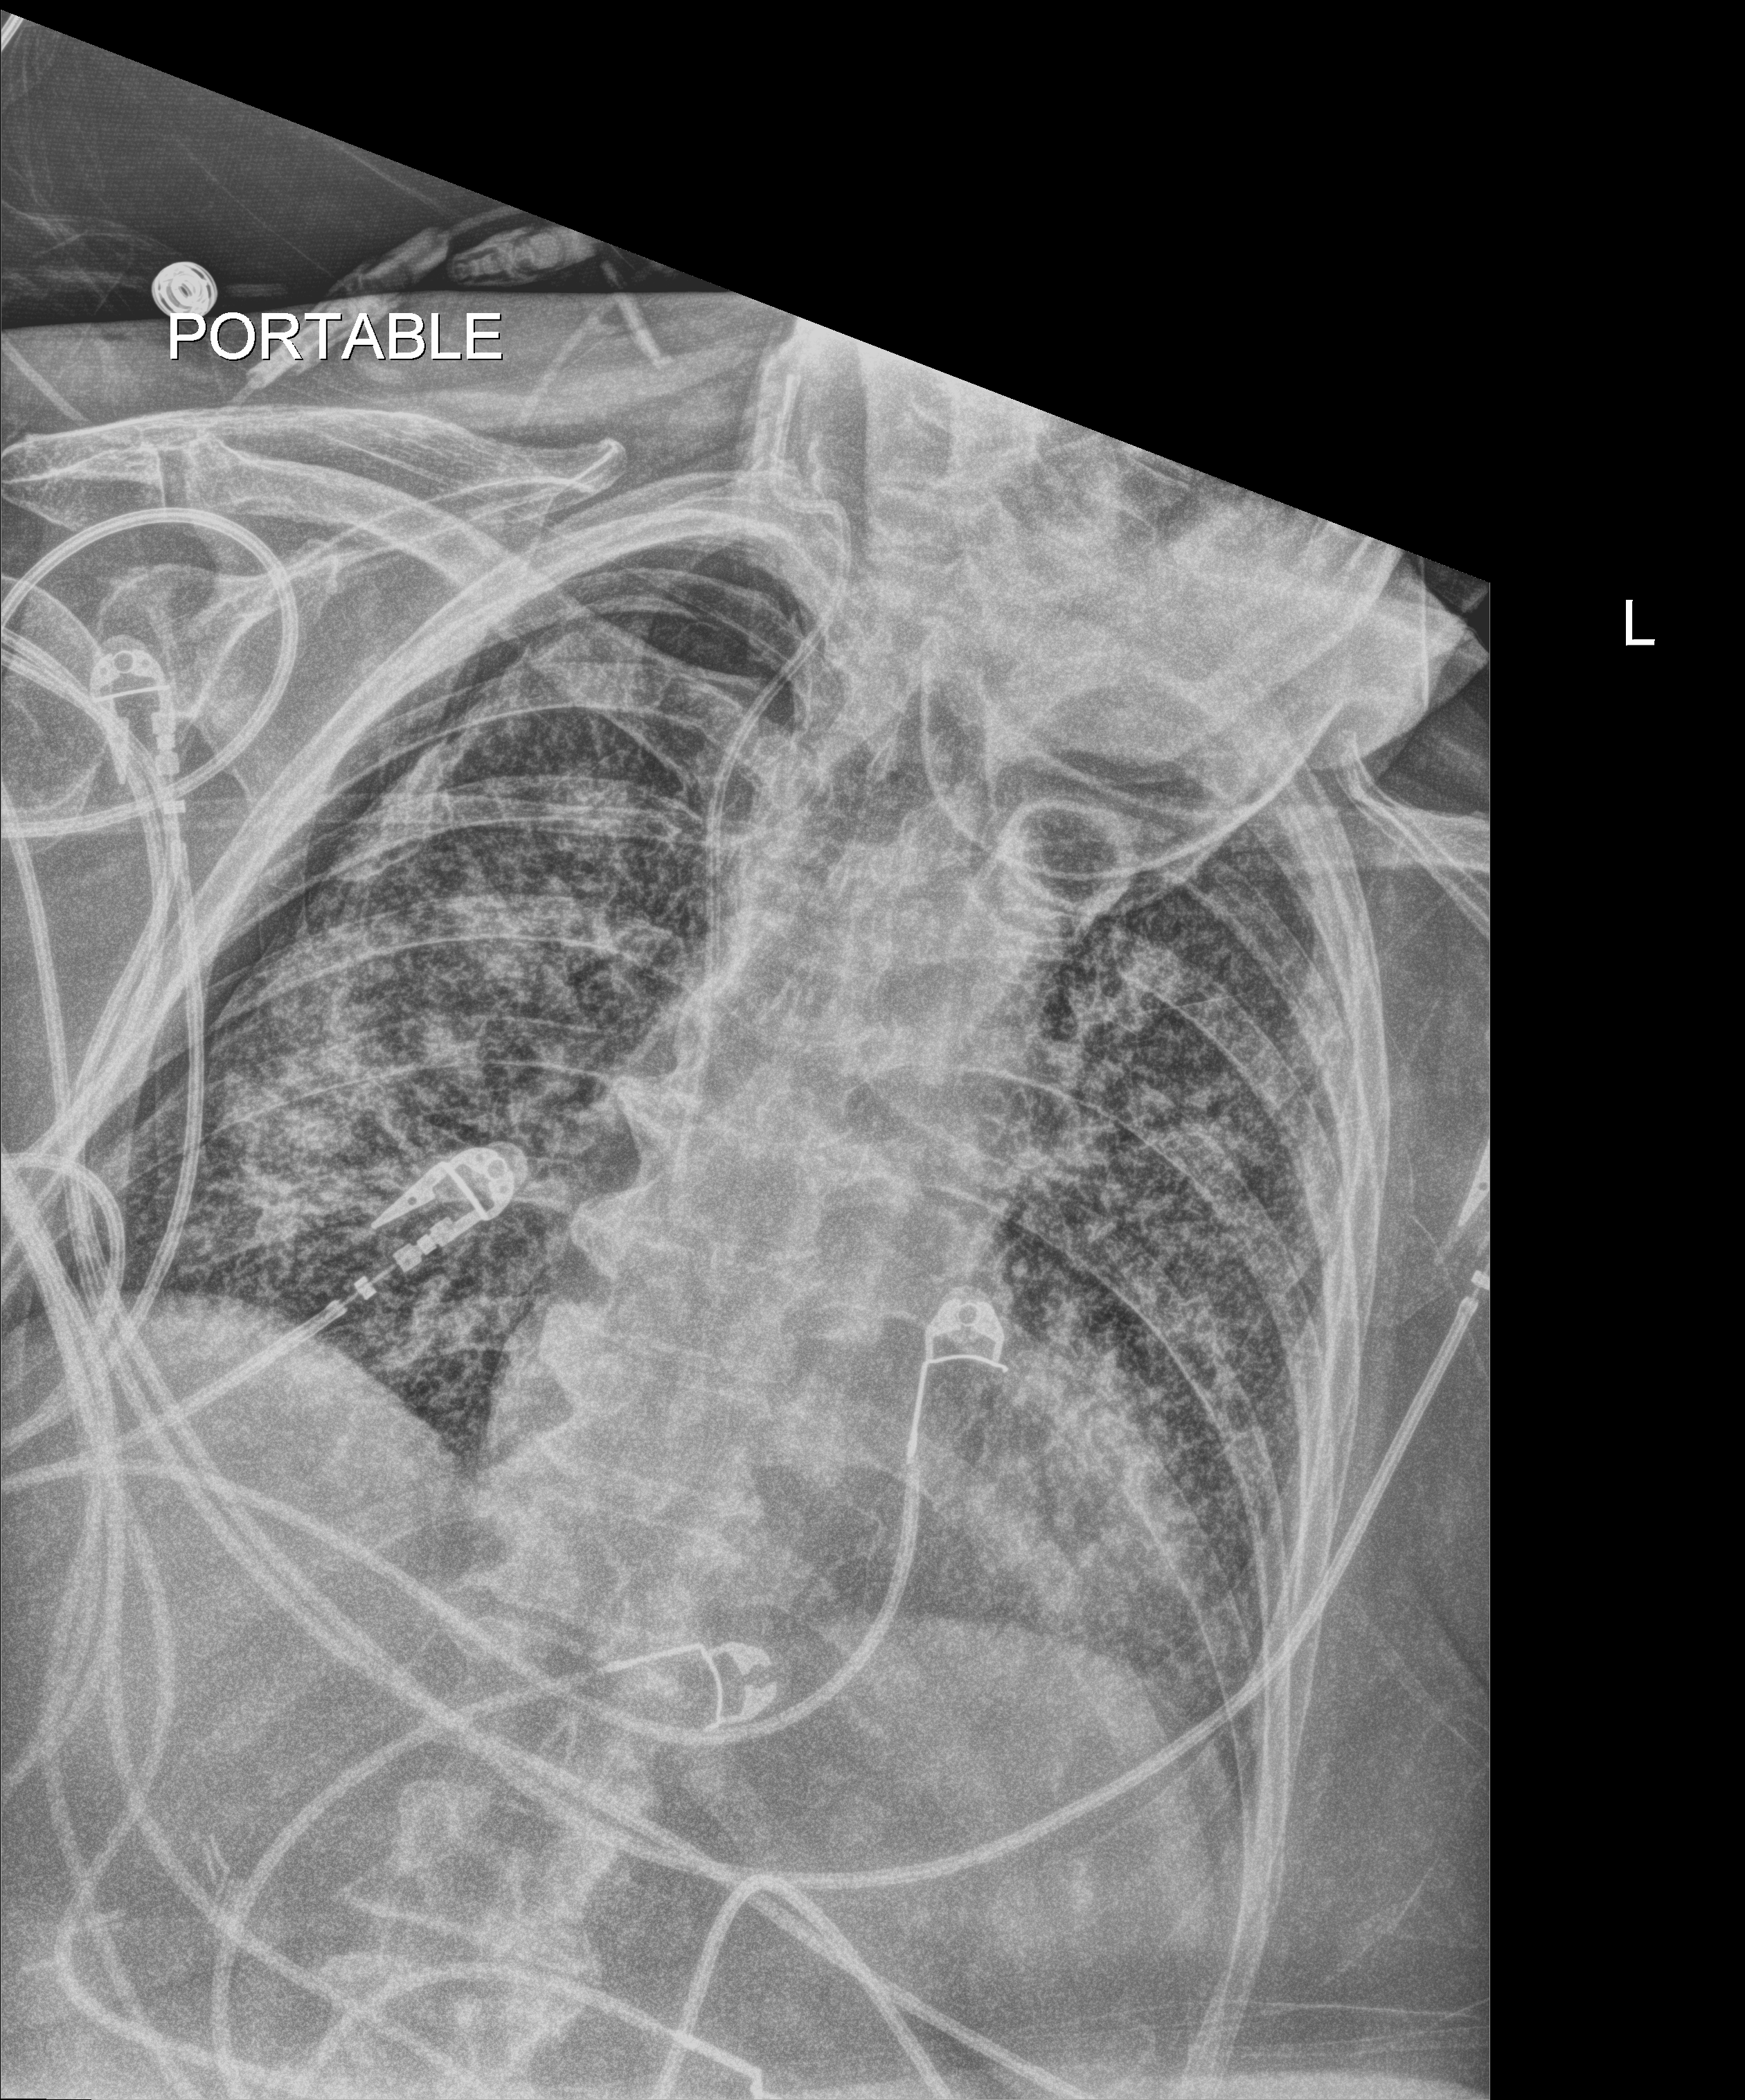
Chest X-ray; anteroposterior (AP) projection. Female patient hospitalised with COVID-19, age 75–90 years.
Hospital-stay facts (about this admission, not read from this image; timing relative to this image not recorded): length of hospital stay: 56 days; admitted to intensive care during this hospital stay: no.